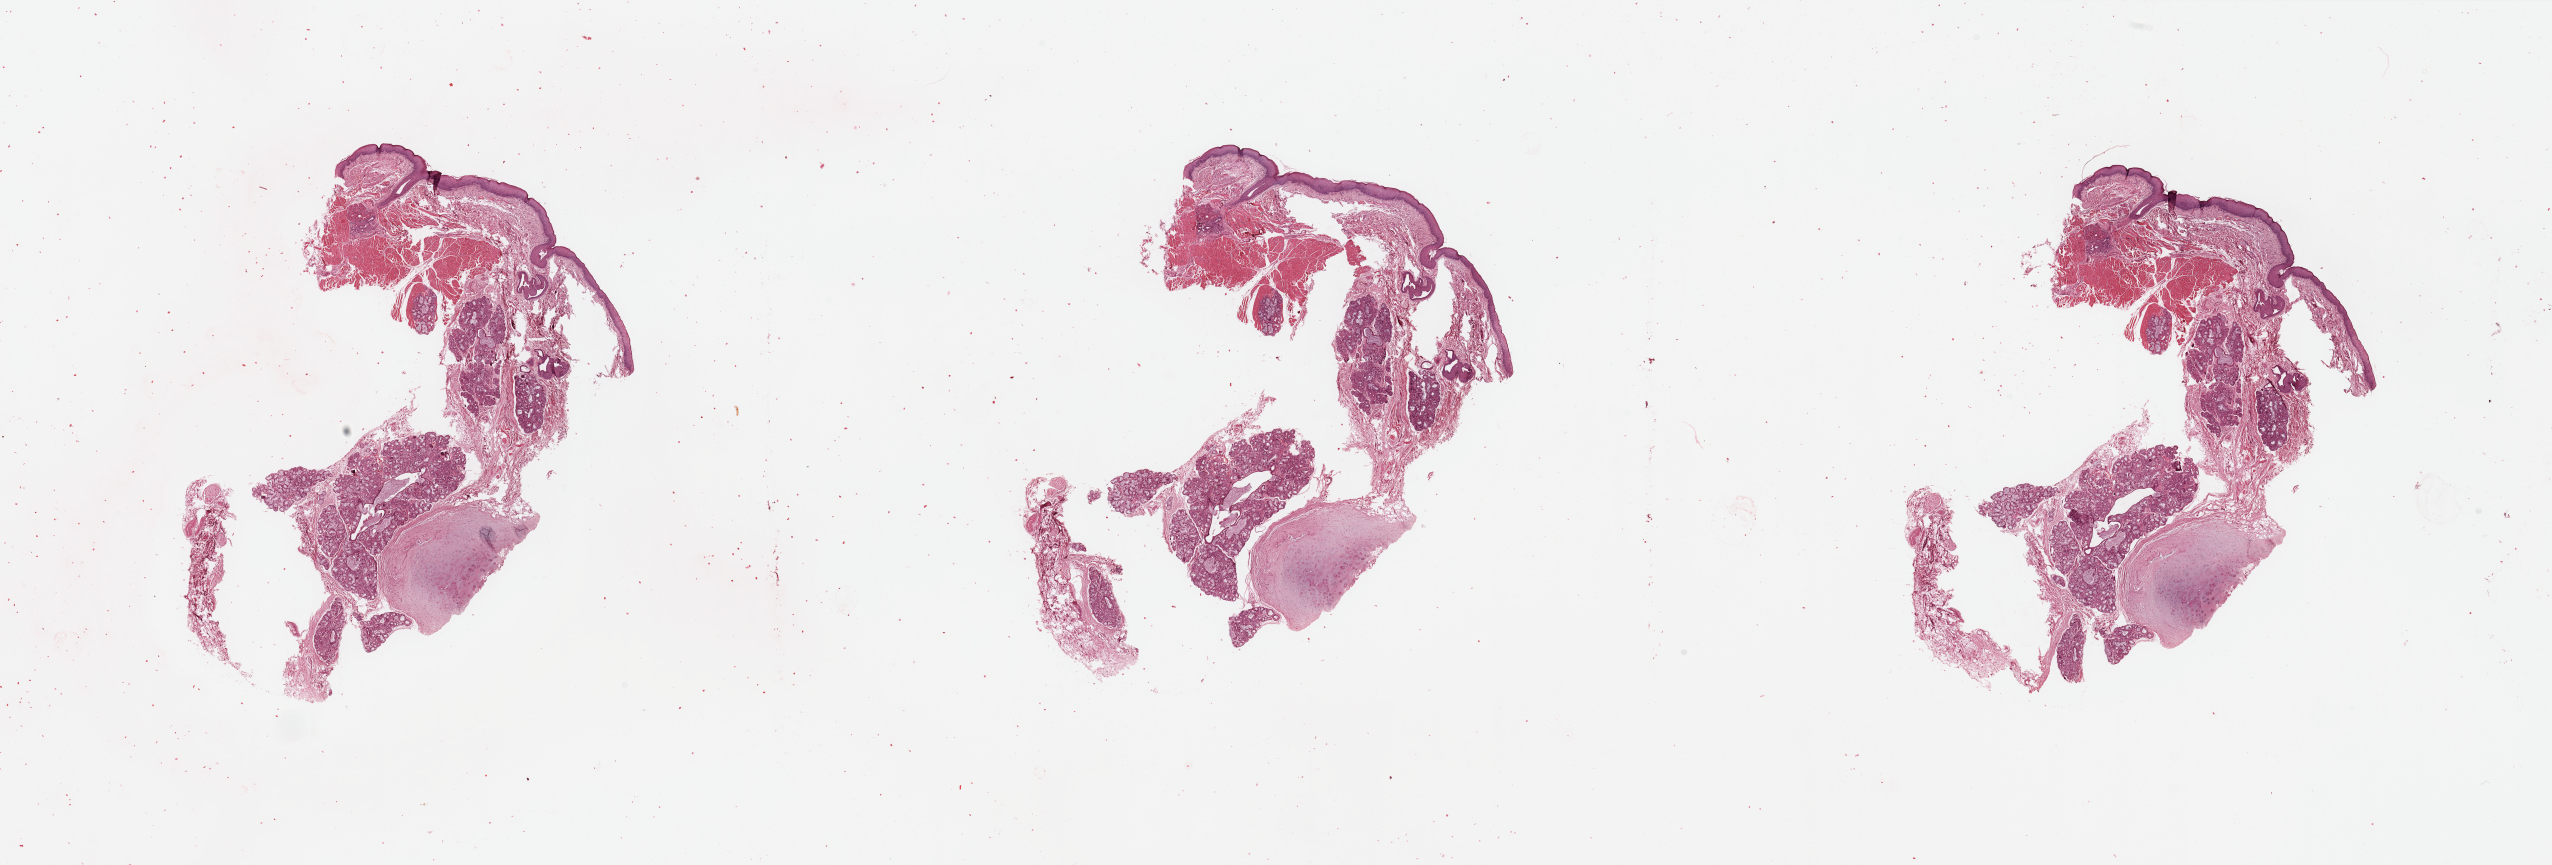
H&E whole-slide image, low-resolution overview of the scanned area, about 40.4 x 13.7 mm; normal (non-tumour) tissue sample, sampled site: larynx. Male, 64 y/o.
This section: normal (non-tumour) tissue from the same patient. Patient diagnosis: Squamous cell carcinoma, NOS (larynx, NOS).